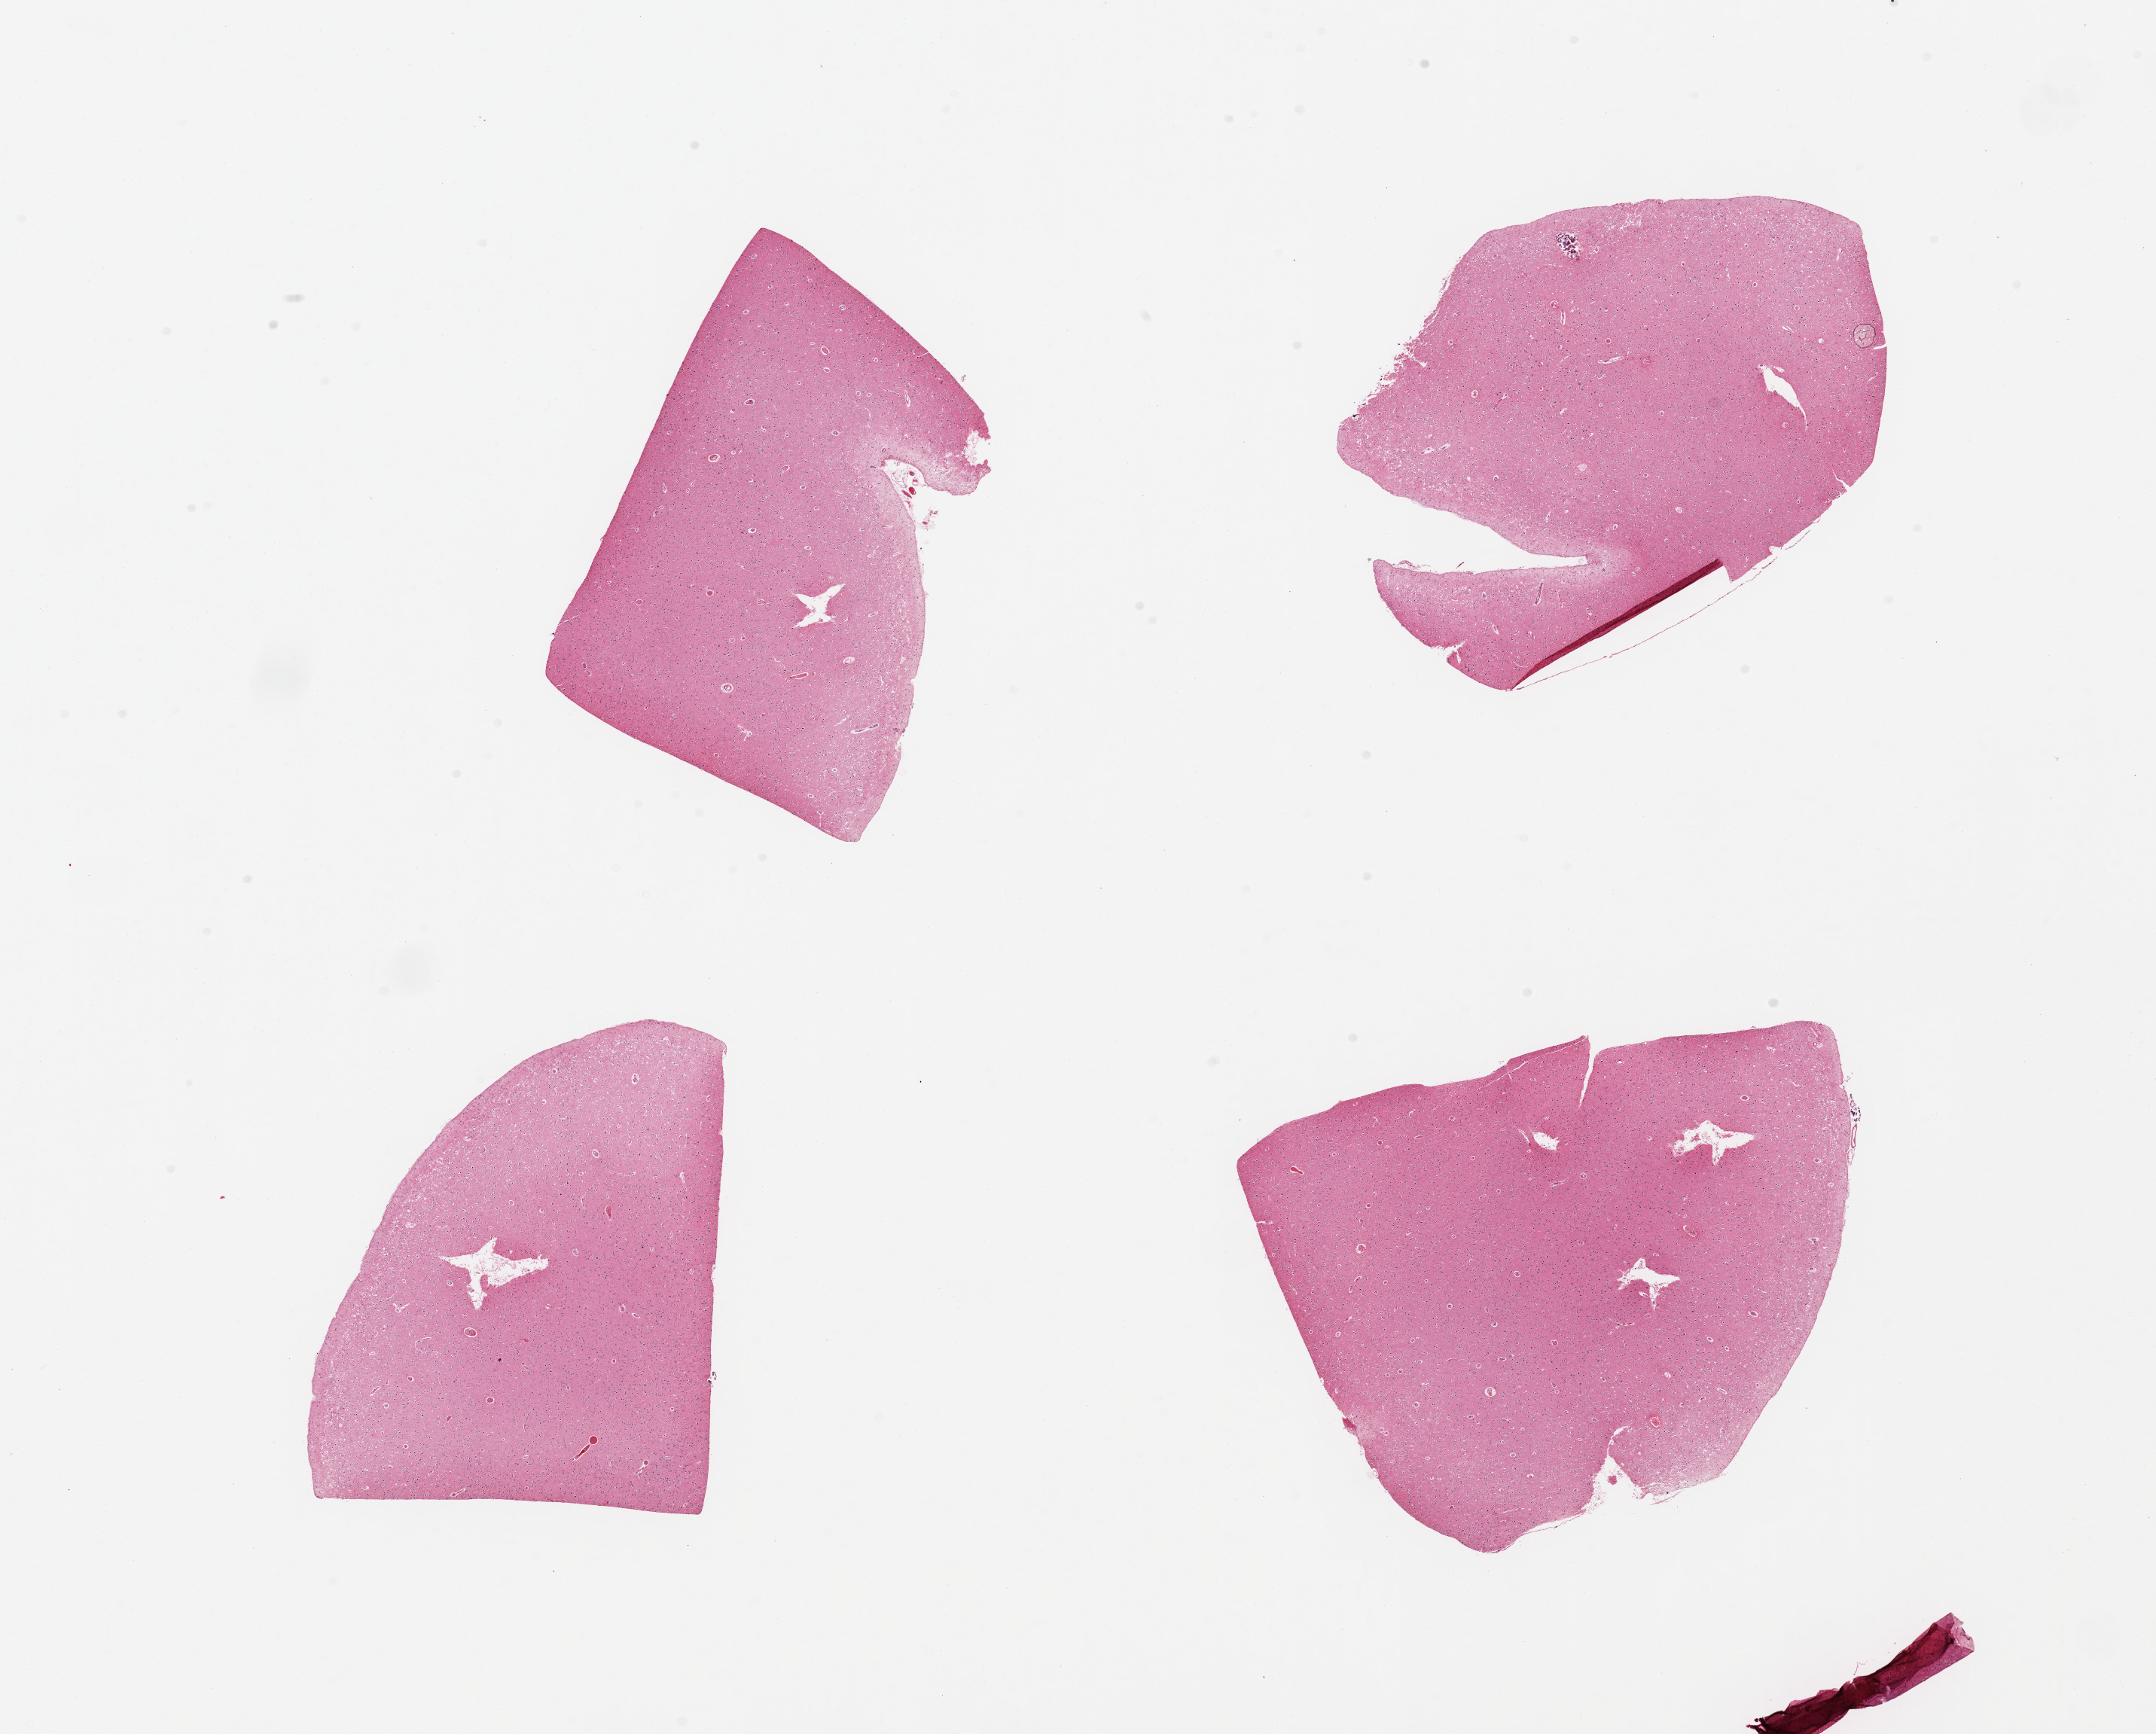
Hematoxylin and eosin (H&E) whole-slide image, low-resolution overview of the scanned area, about 22.6 x 18.2 mm. PAXgene-fixed paraffin-embedded (PFPE) section. Section of cerebral cortex (target tissue). Donor tissue sample. Donor: male.
Pathologist's review note for this sample: 4 pieces; mild to moderate autolysis.